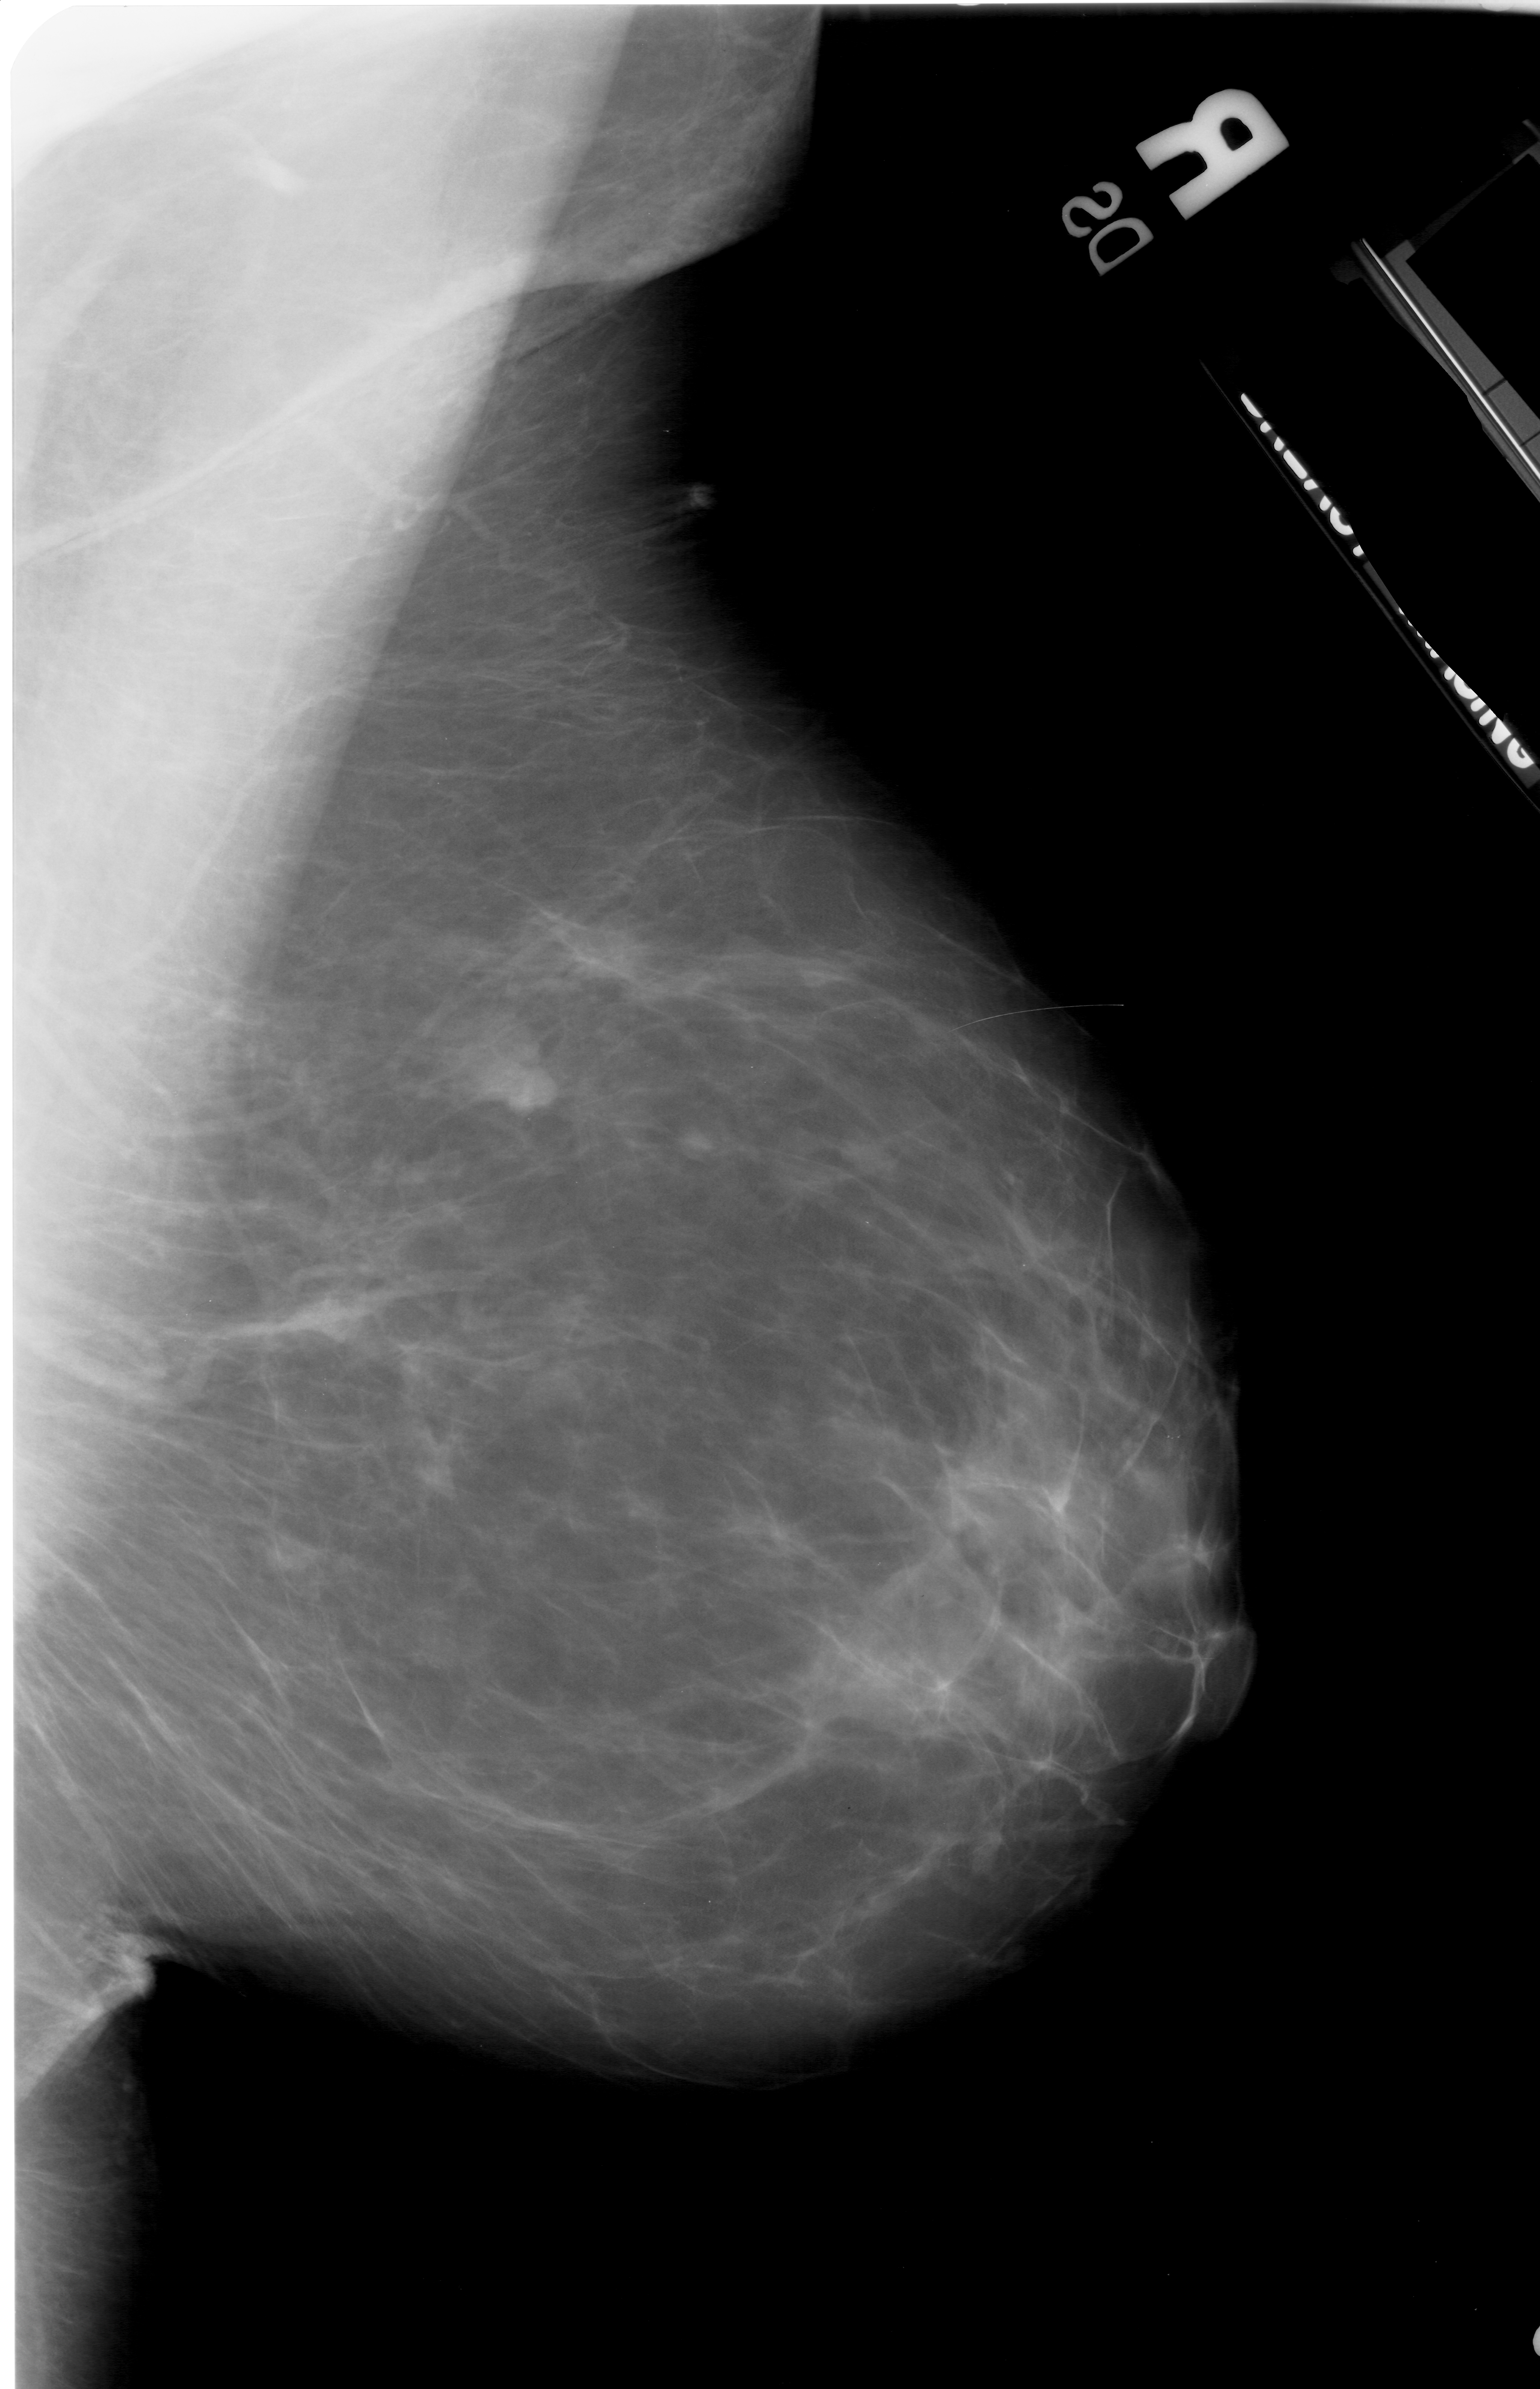
Mammogram (digitized film), right breast, mediolateral oblique (MLO) view, BI-RADS breast density category 1 (scale 1–4).
Marked abnormality: mass, shape lobulated, margins obscured; BI-RADS assessment category 3; subtlety rating 4 on a 1 (subtle) to 5 (obvious) scale; pathology (as recorded): benign.